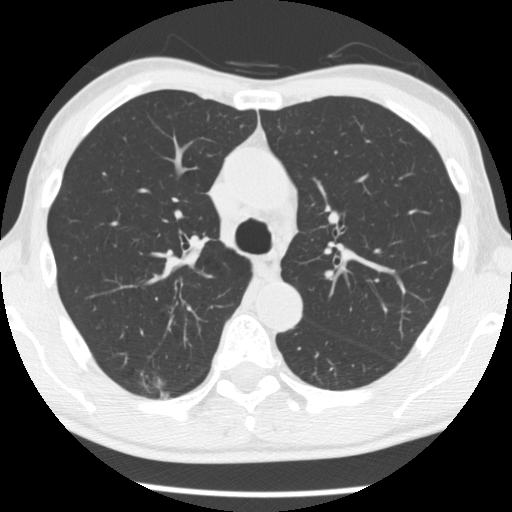
Chest CT (low-dose screening protocol), one axial image. First (baseline) screen. Lung window (W 1500 / L -600 HU). 2.5 mm slice thickness. Male participant, aged 66 years at enrolment. Former smoker at enrolment.
Expert reader's lesion annotation, bounding box <128,356,192,407> (left, top, right, bottom; pixels). The screening reader recorded 4 non-calcified nodules or masses ≥4 mm on this exam (right upper lobe, right upper lobe, right upper lobe, left lower lobe); which of them this box marks is not recorded. Official screen result: positive, change unspecified: nodule(s) >= 4 mm or enlarging nodule(s), mass(es), or other non-specific abnormalities suspicious for lung cancer.